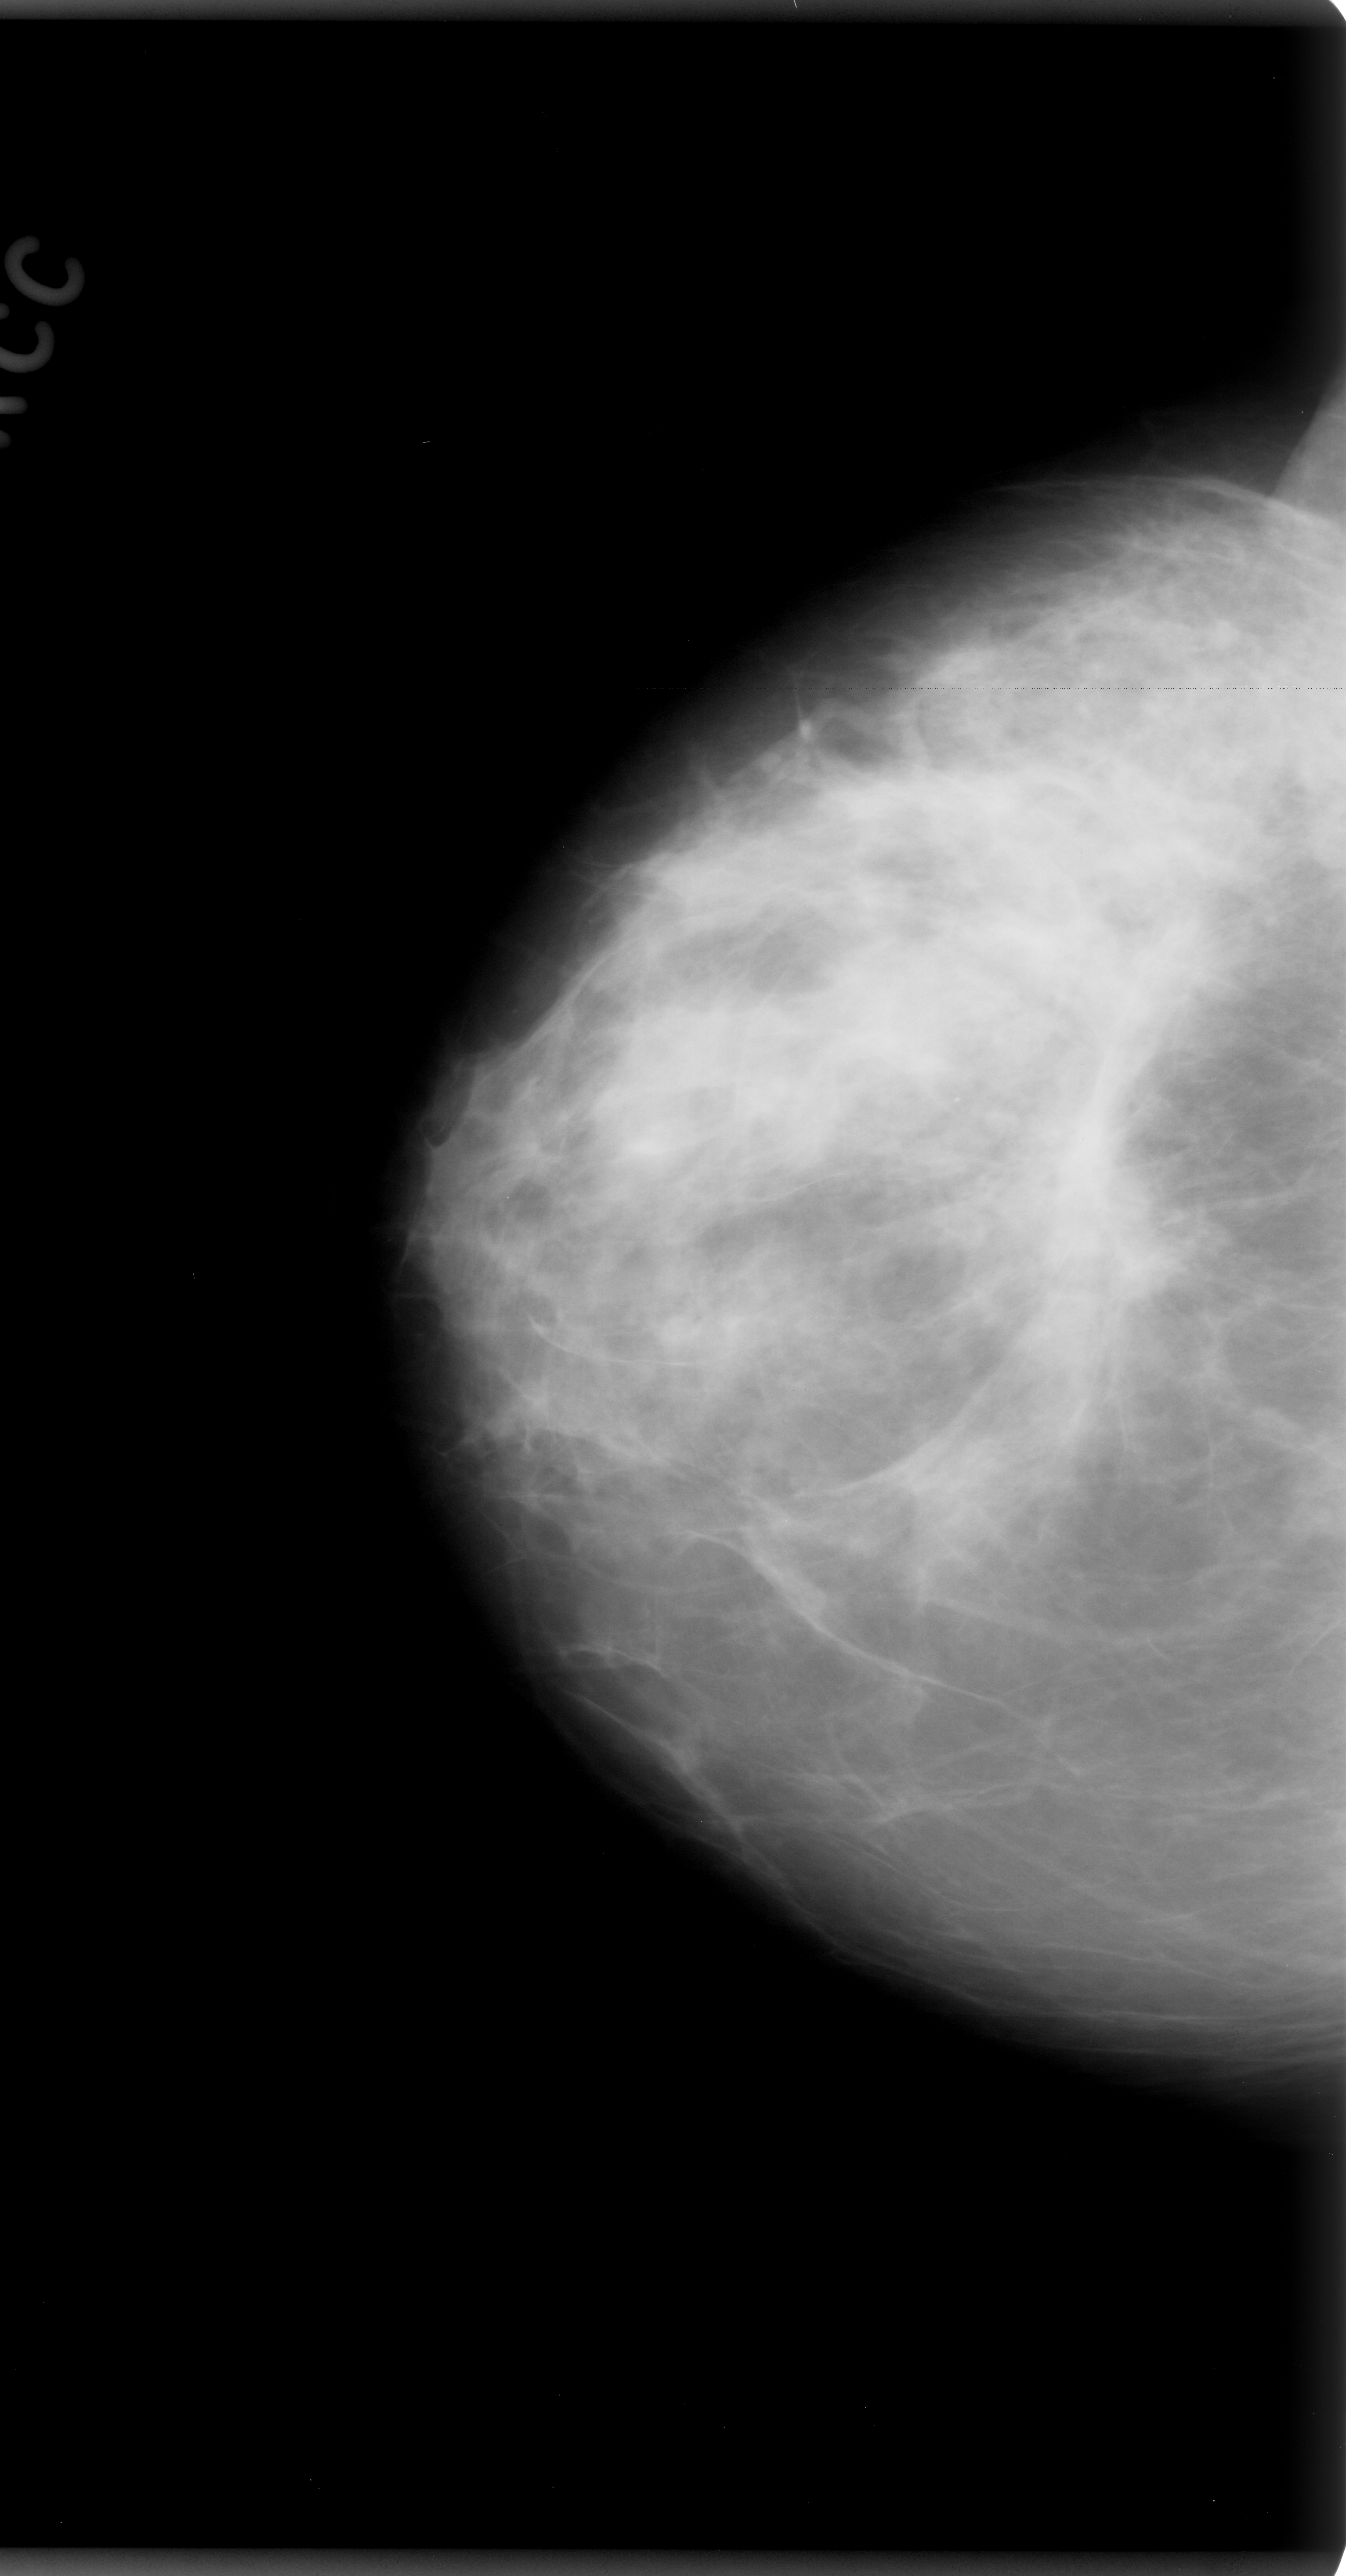
Digitized screen-film mammogram; right breast; craniocaudal (CC) view; 1346 × 2576 image matrix.
Expert-marked regions of interest on this film, with their recorded descriptors:
- mass, shape architectural distortion, margins spiculated; BI-RADS assessment category 5; pathology result (as recorded, not read from the image): malignant: bounding box (x1, y1, x2, y2) in pixels: (1000, 1089, 1208, 1306)